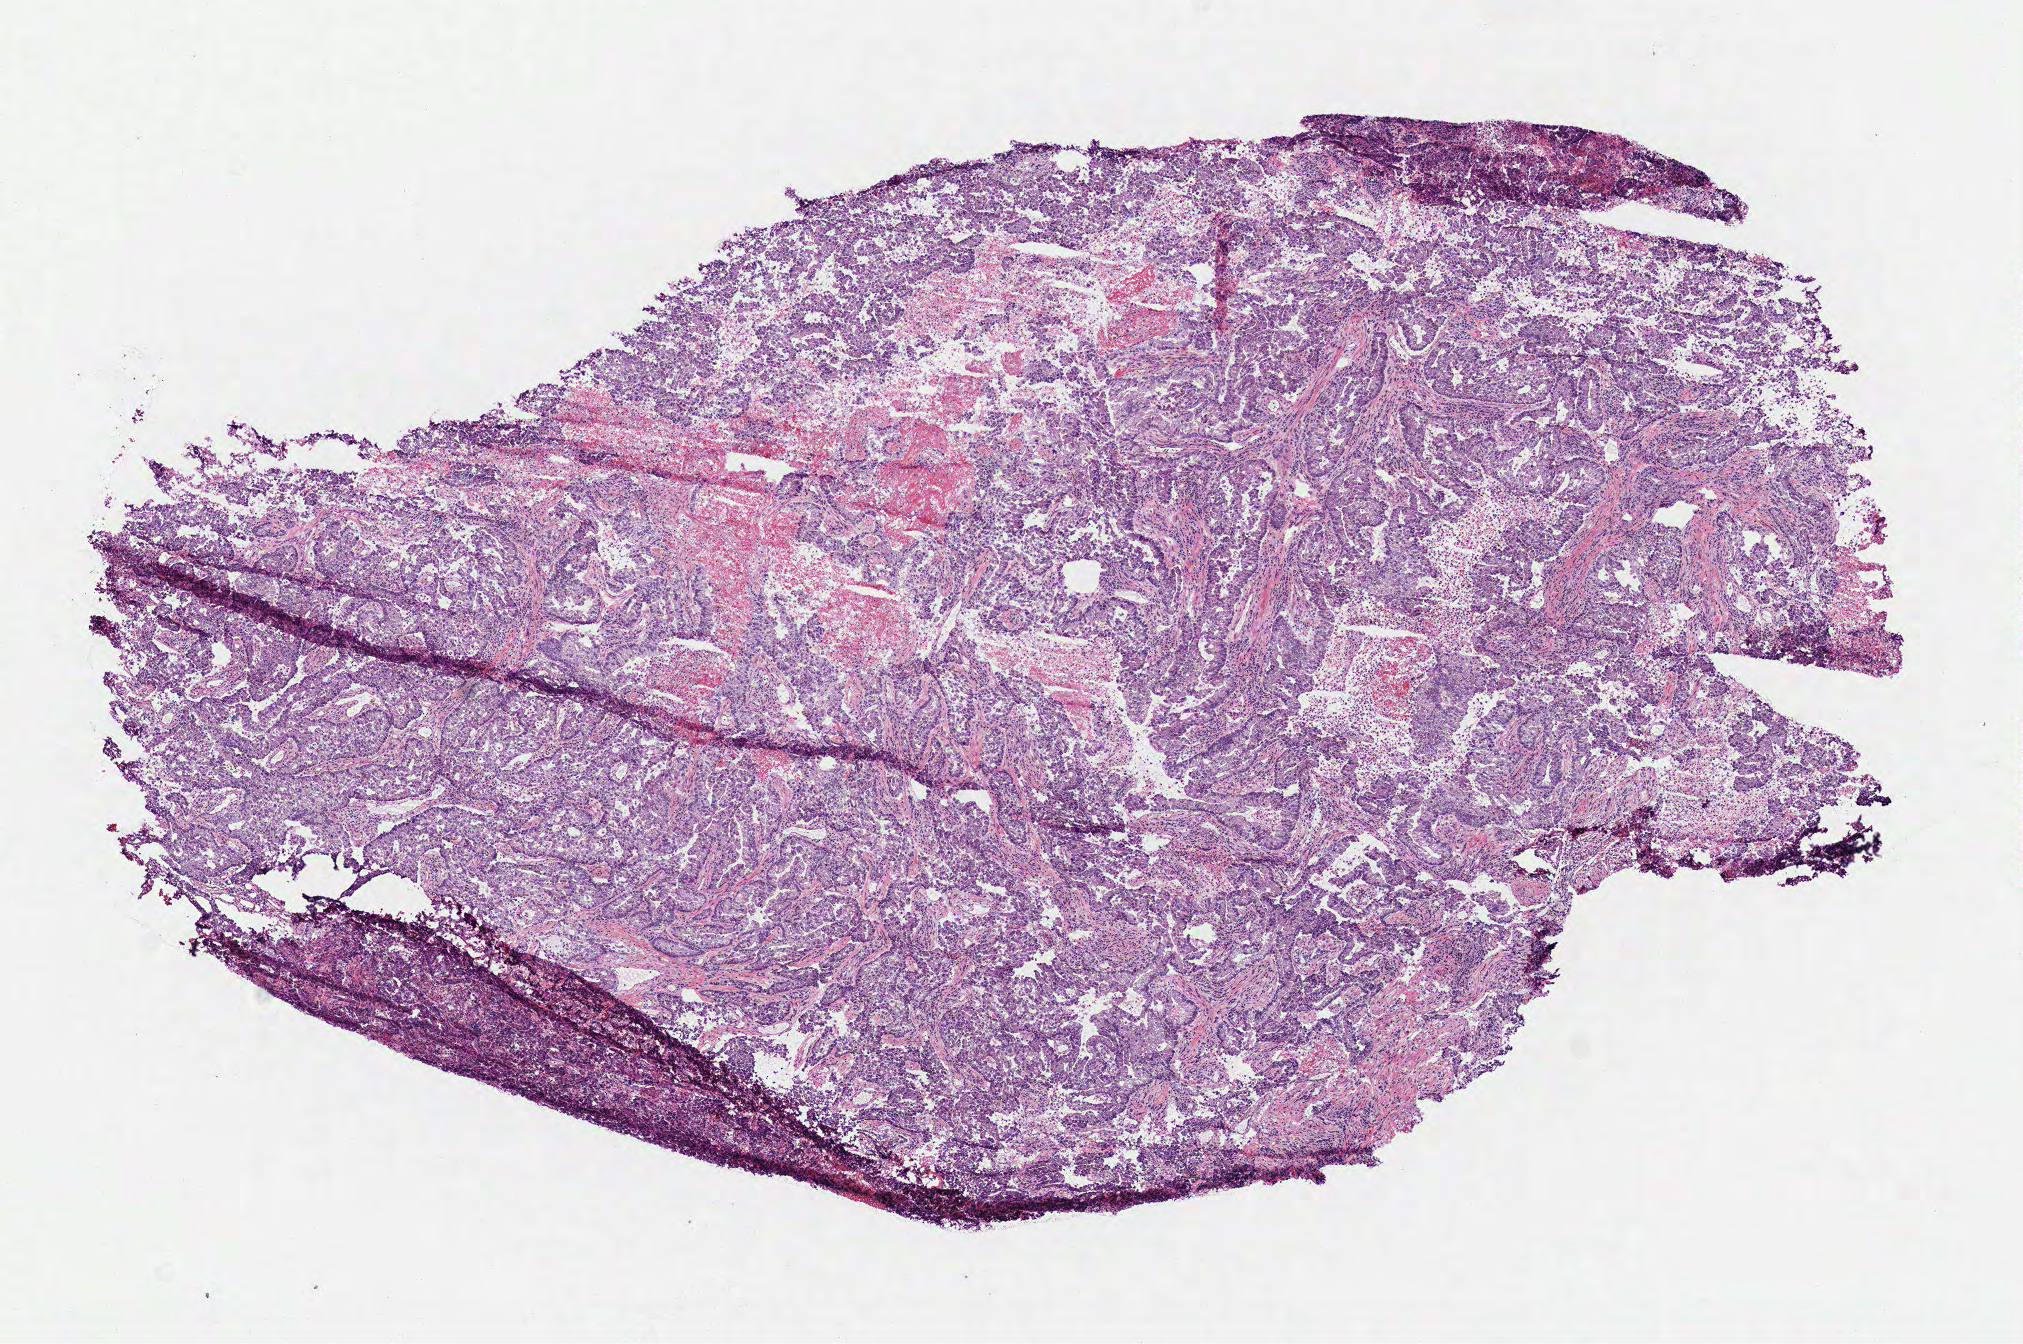
Whole-slide histology image, Hematoxylin and eosin (H&E) stained, a low-resolution overview of the entire scanned area, about 8.0 x 5.3 mm. Frozen section from the bottom of the tissue portion. Lung, primary tumour sample. Female, age 60 years at initial diagnosis. Pathologist review of this section (percent, as recorded): tumour cells 75%, tumour nuclei 70%, normal cells 0%, stromal cells 10%, necrosis 15%.
- TNM: T1 NX M0
- AJCC pathologic stage: IA (6th edition)
- diagnosis: Adenocarcinoma with mixed subtypes (upper lobe, lung)